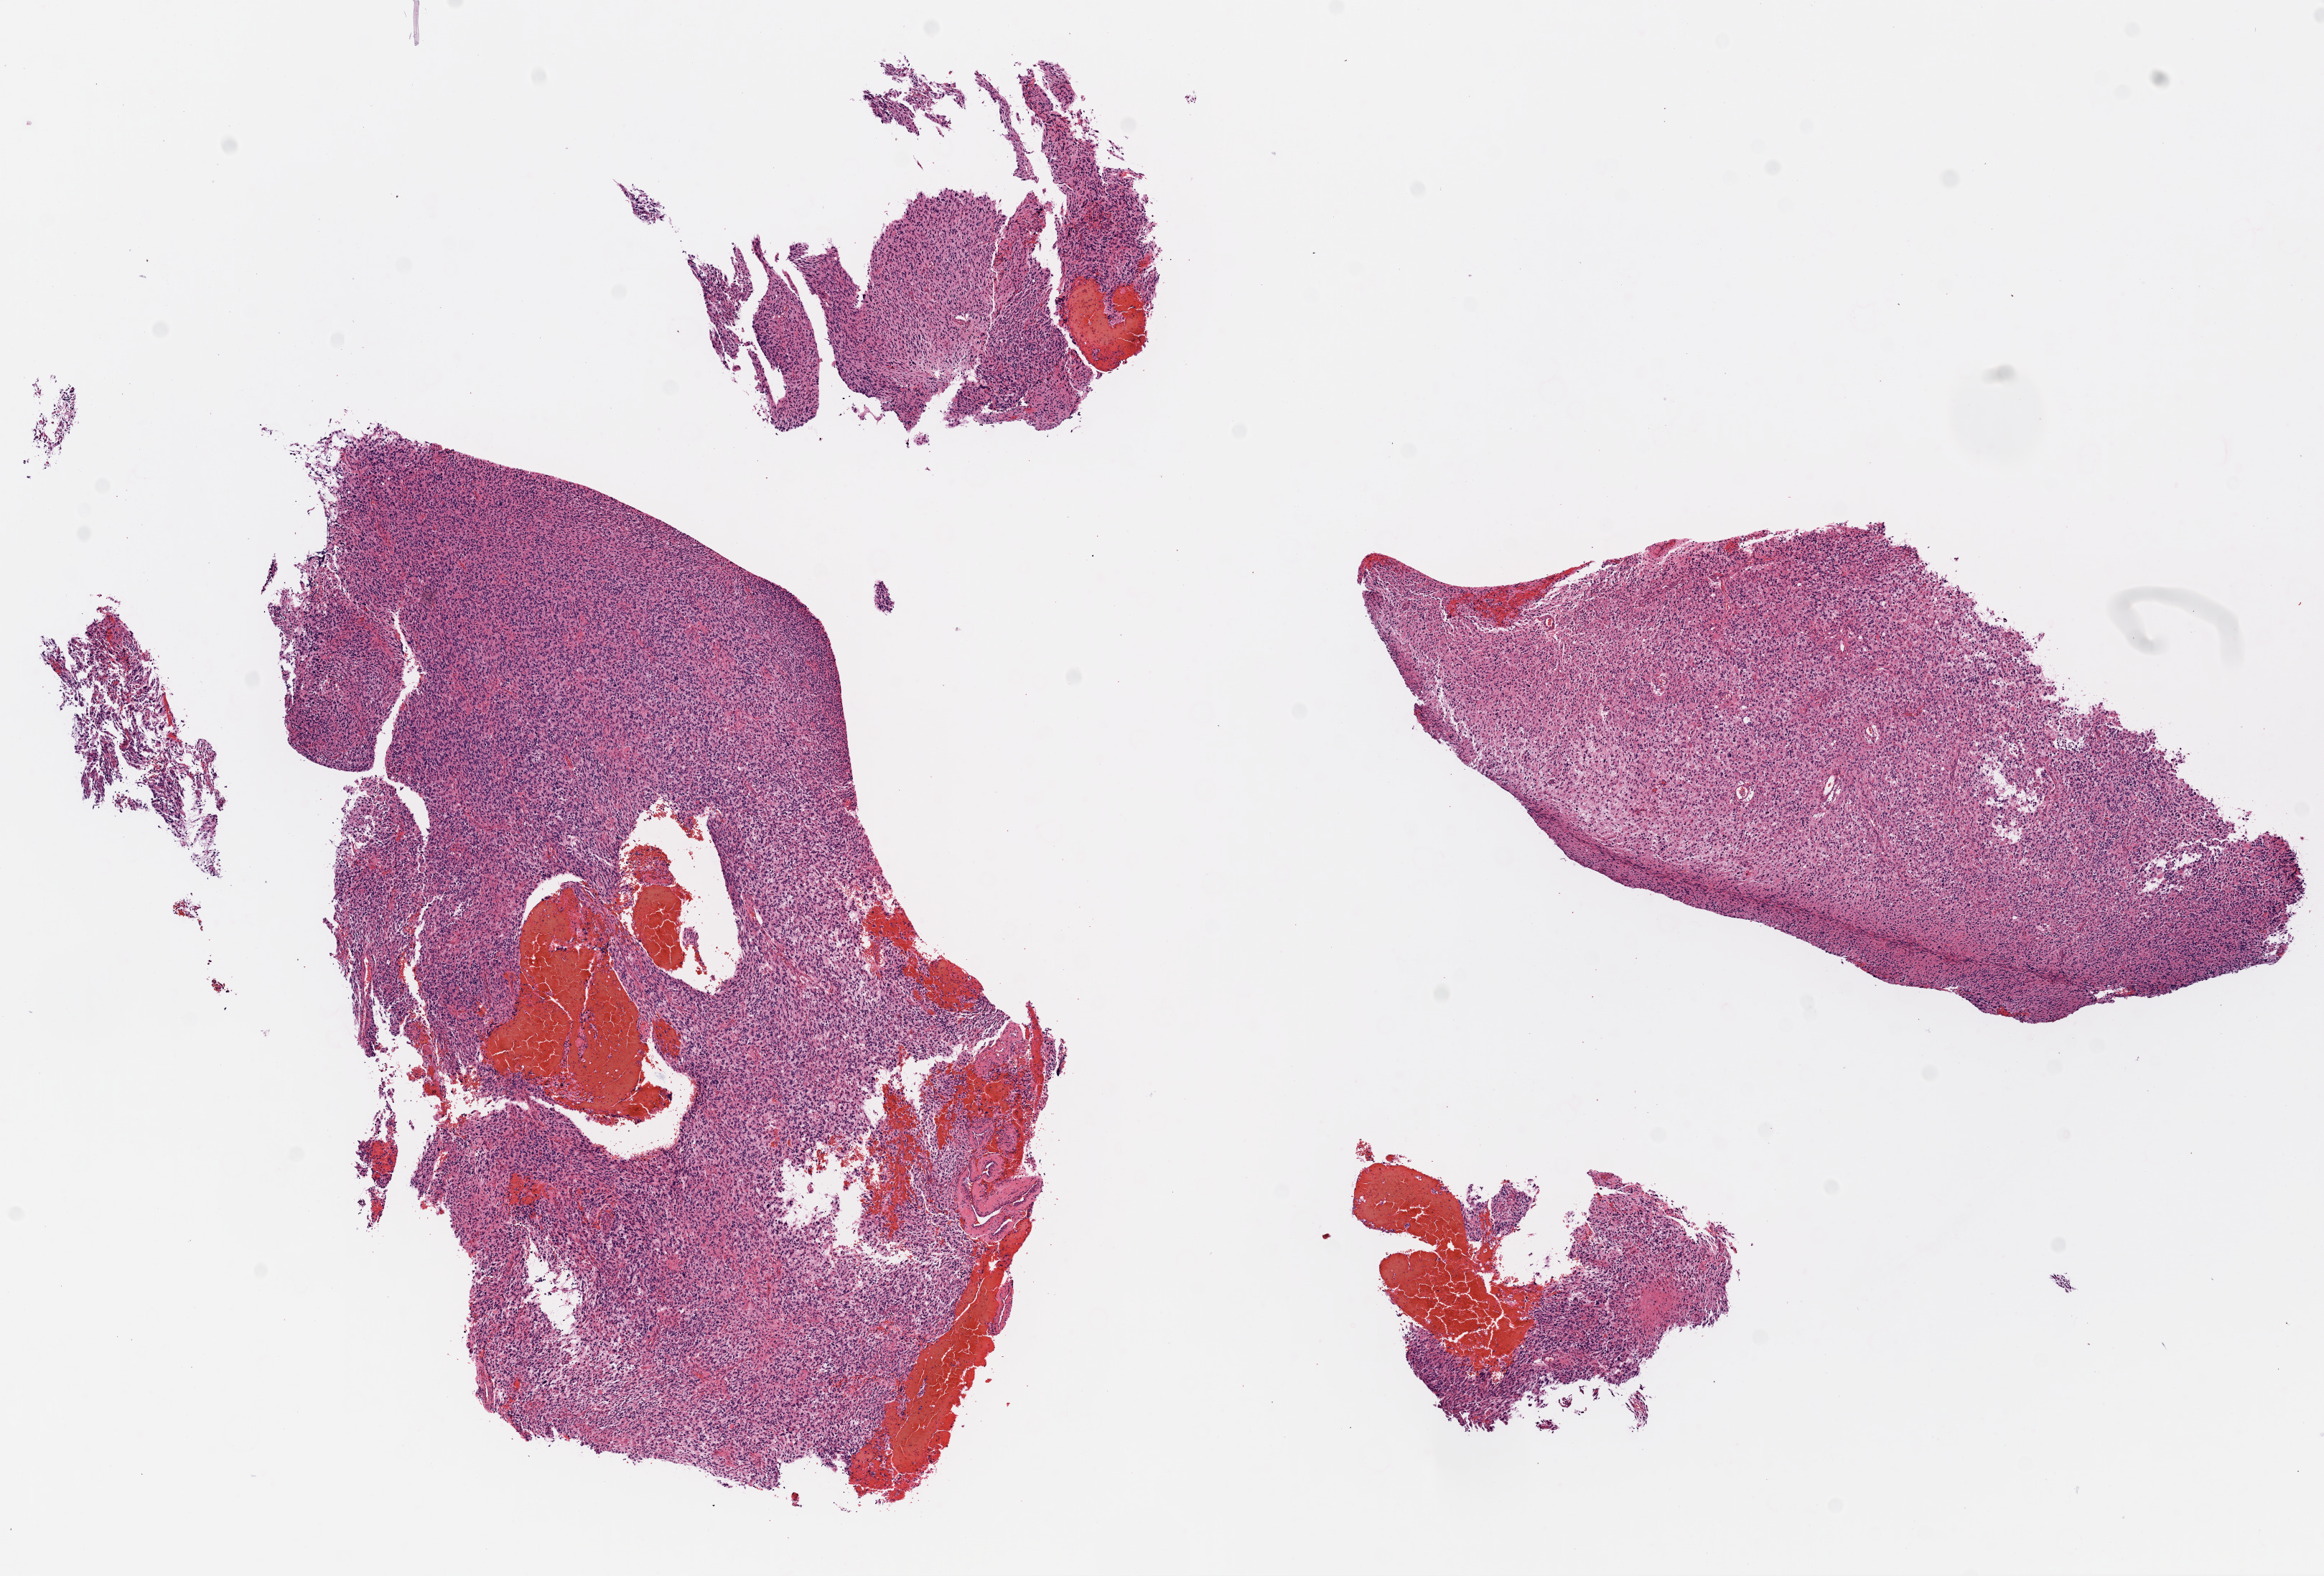
Whole-slide histology image, H&E — low-resolution overview of the scanned area, about 13.1 x 8.9 mm (acquisition: 20x scan); FFPE section; sample: primary tumour, brain. Patient: male, age at initial diagnosis 31 years.
Diagnosis: Glioblastoma.